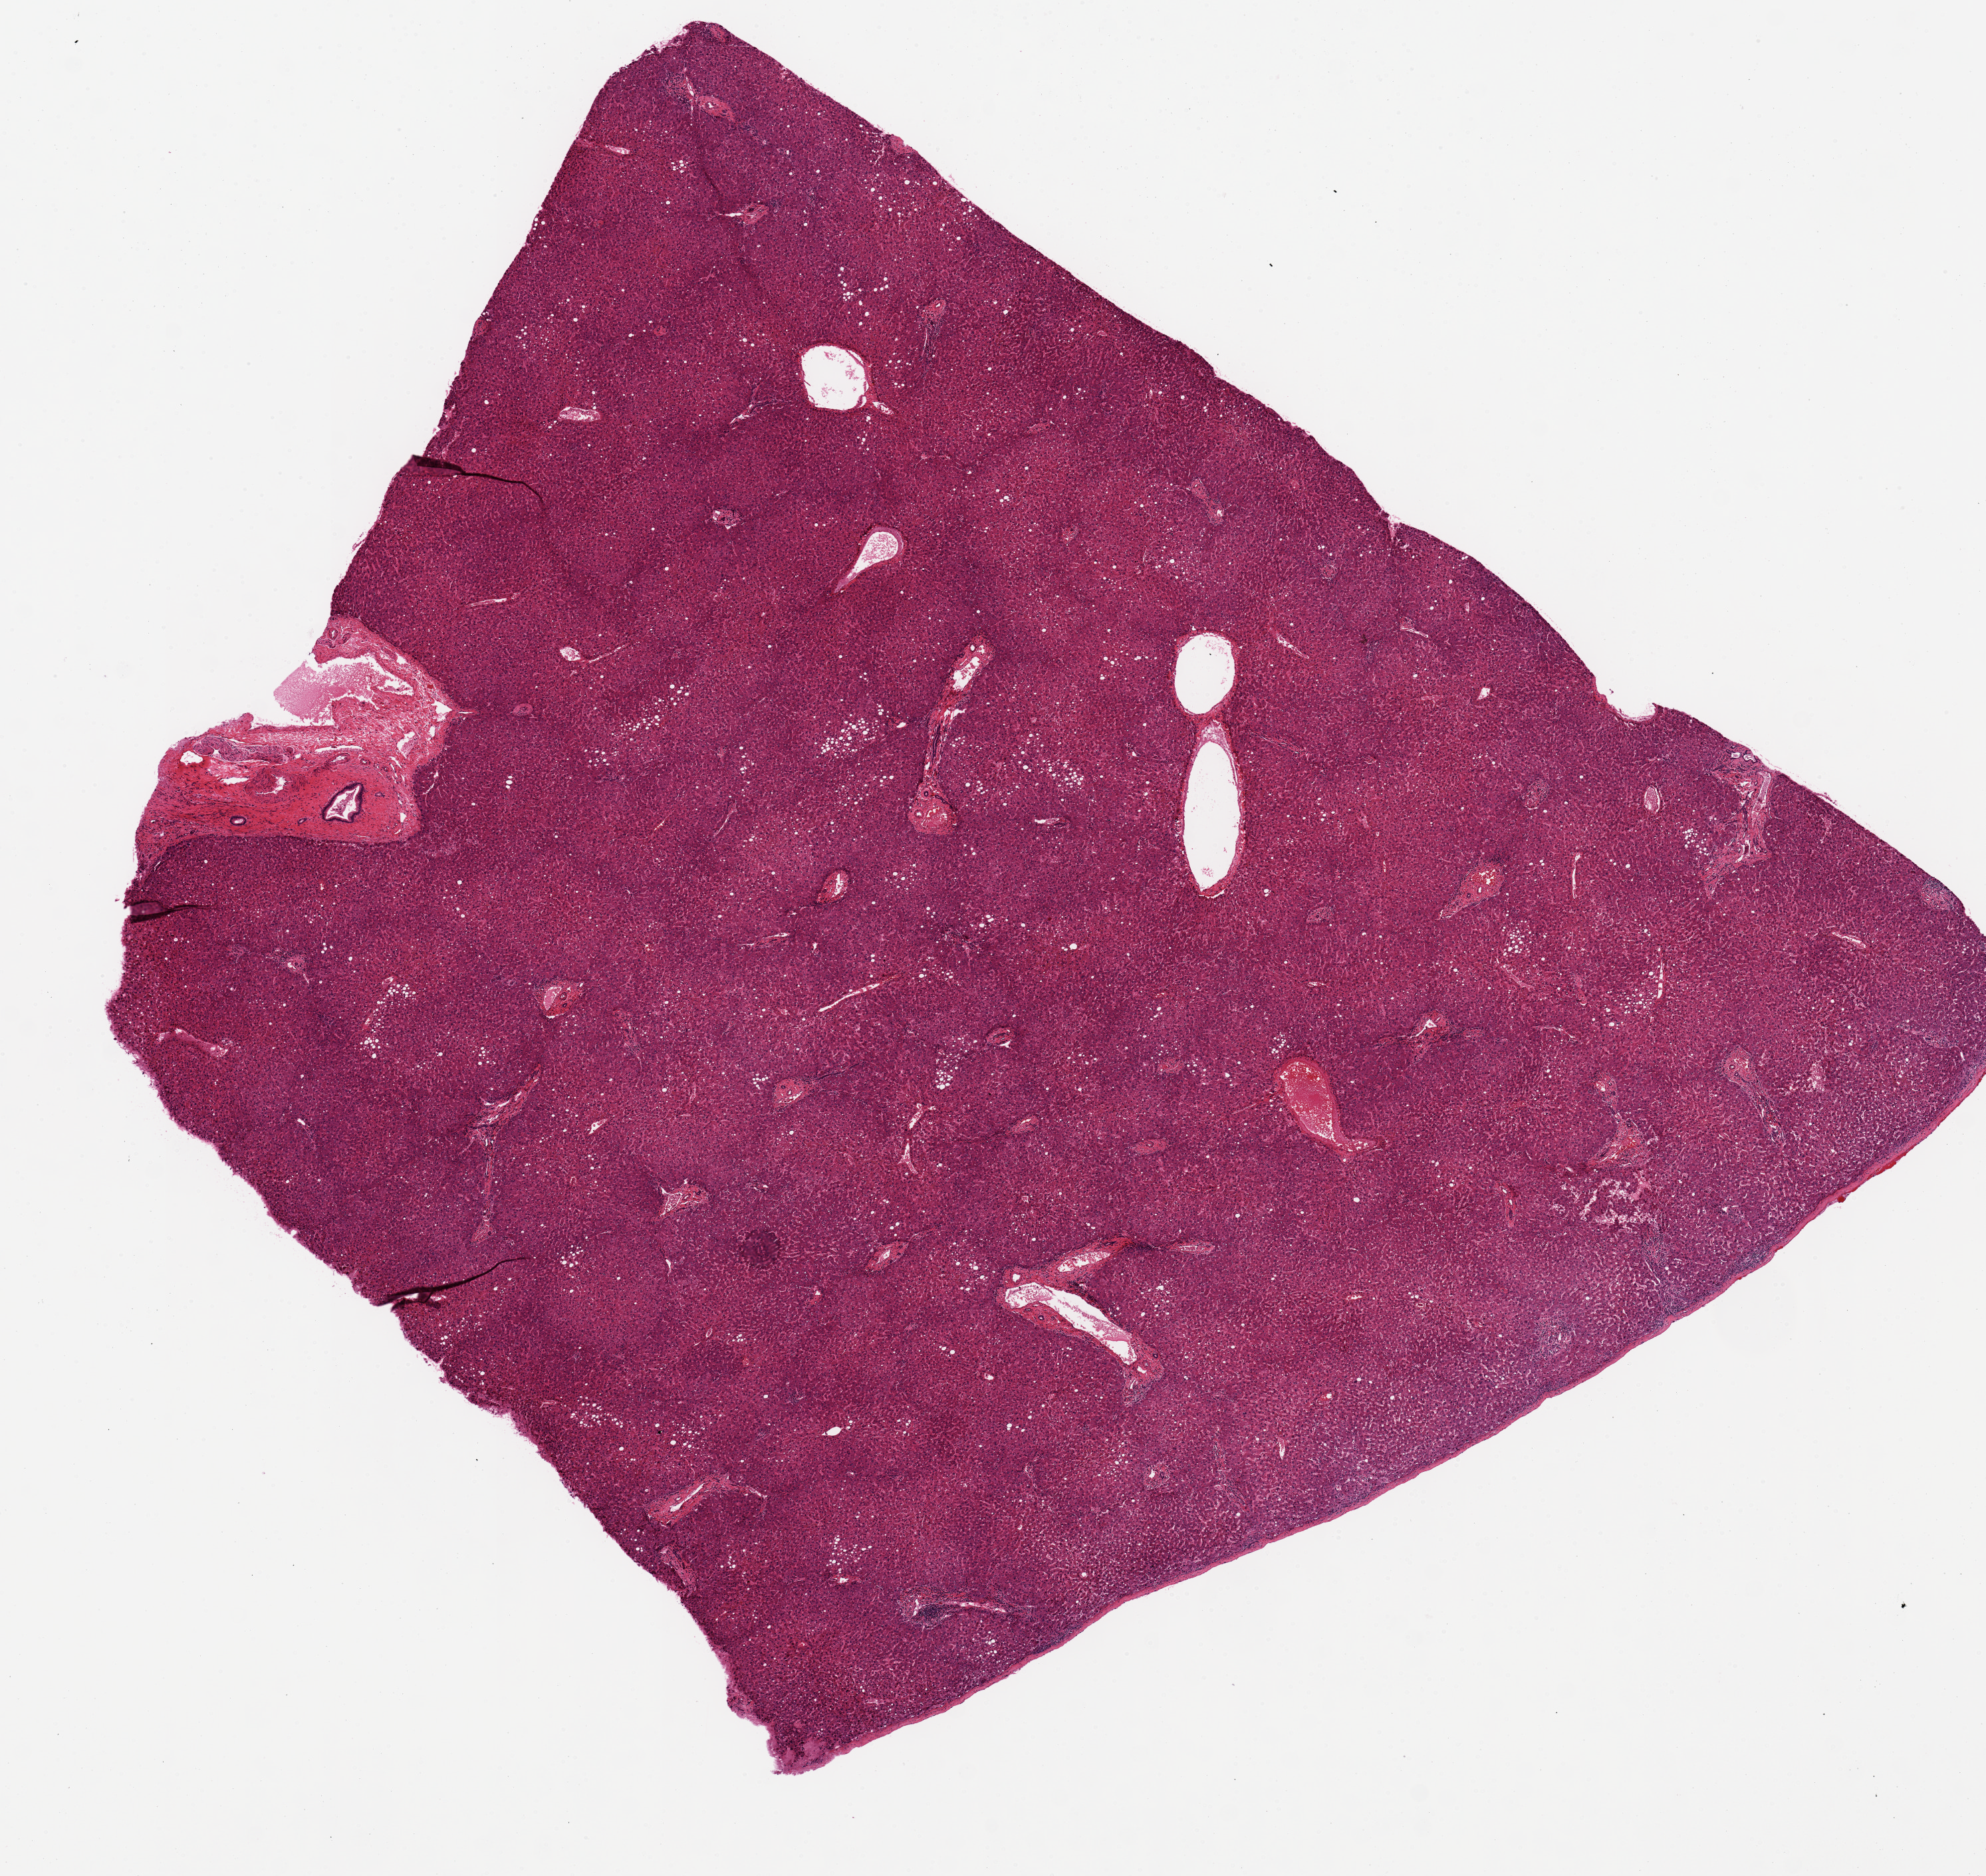
Hematoxylin and eosin (H&E) whole-slide image, shown as a low-resolution overview of the whole scanned area (about 11.8 x 11.2 mm); PAXgene-fixed paraffin-embedded (PFPE) section; target tissue: liver; tissue donor sample. Female donor.
• reviewer comment on this tissue sample: Mild macrovesicluarsteatosis. Aliquot contains liver capsule